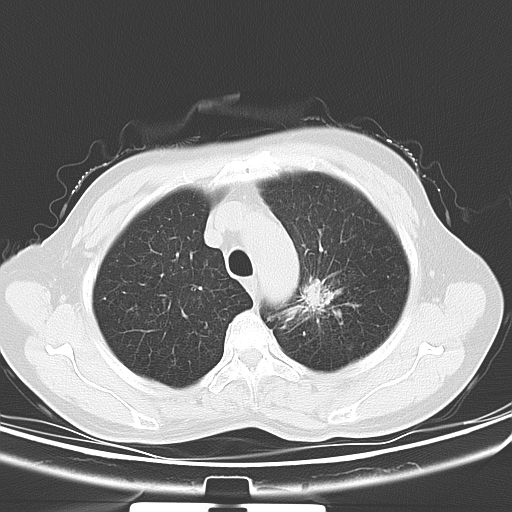
Chest CT, one axial slice; slice 45 of 53 in the series (ordered by position); 120 kVp; lung window (W 1500 / L -600 HU); 512 × 512 image matrix, field of view 329 × 329 mm. Patient: female, 60 years. Case-level facts recorded for this patient, not image findings: clinical TNM (as recorded): T1b N0 M0.
Outlined on this slice (bounding box drawn by a radiologist):
- lung tumour (recorded histology: squamous cell carcinoma): bounding box [x1, y1, x2, y2] px = [301, 271, 338, 318]